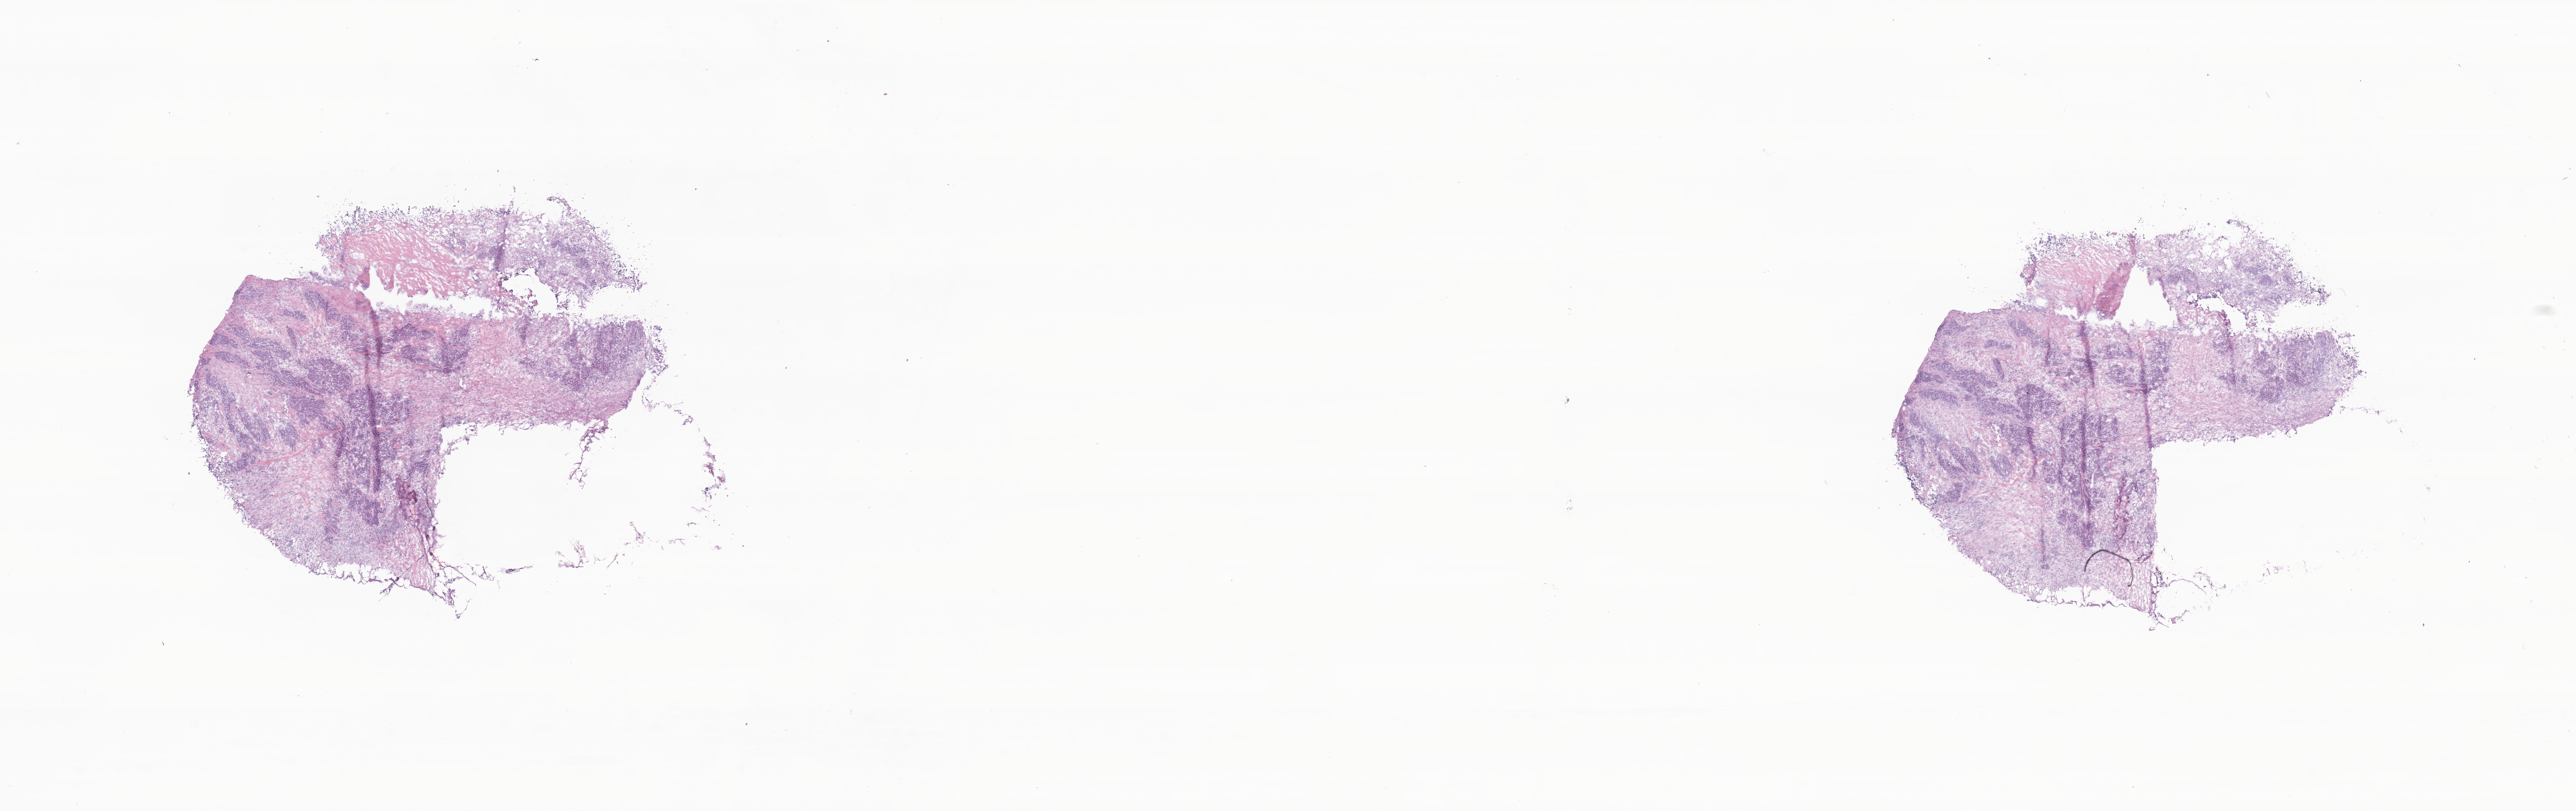
Hematoxylin and eosin (H&E) whole-slide image, low-resolution overview of the scanned area, about 25.5 x 8.0 mm, cryosection, primary tumor, site: breast (right). Patient: female, age at initial diagnosis 77 years. Composition of this section per pathologist review: tumor cells 33%, tumor nuclei 75%, stromal cells 64%, necrosis 3%, normal cells 0%. Infiltration values recorded for this section: lymphocyte infiltration 18%, monocyte infiltration 2%, neutrophil infiltration 0%.
Histologic diagnosis: Infiltrating duct carcinoma, NOS. Section: top of the tissue portion.